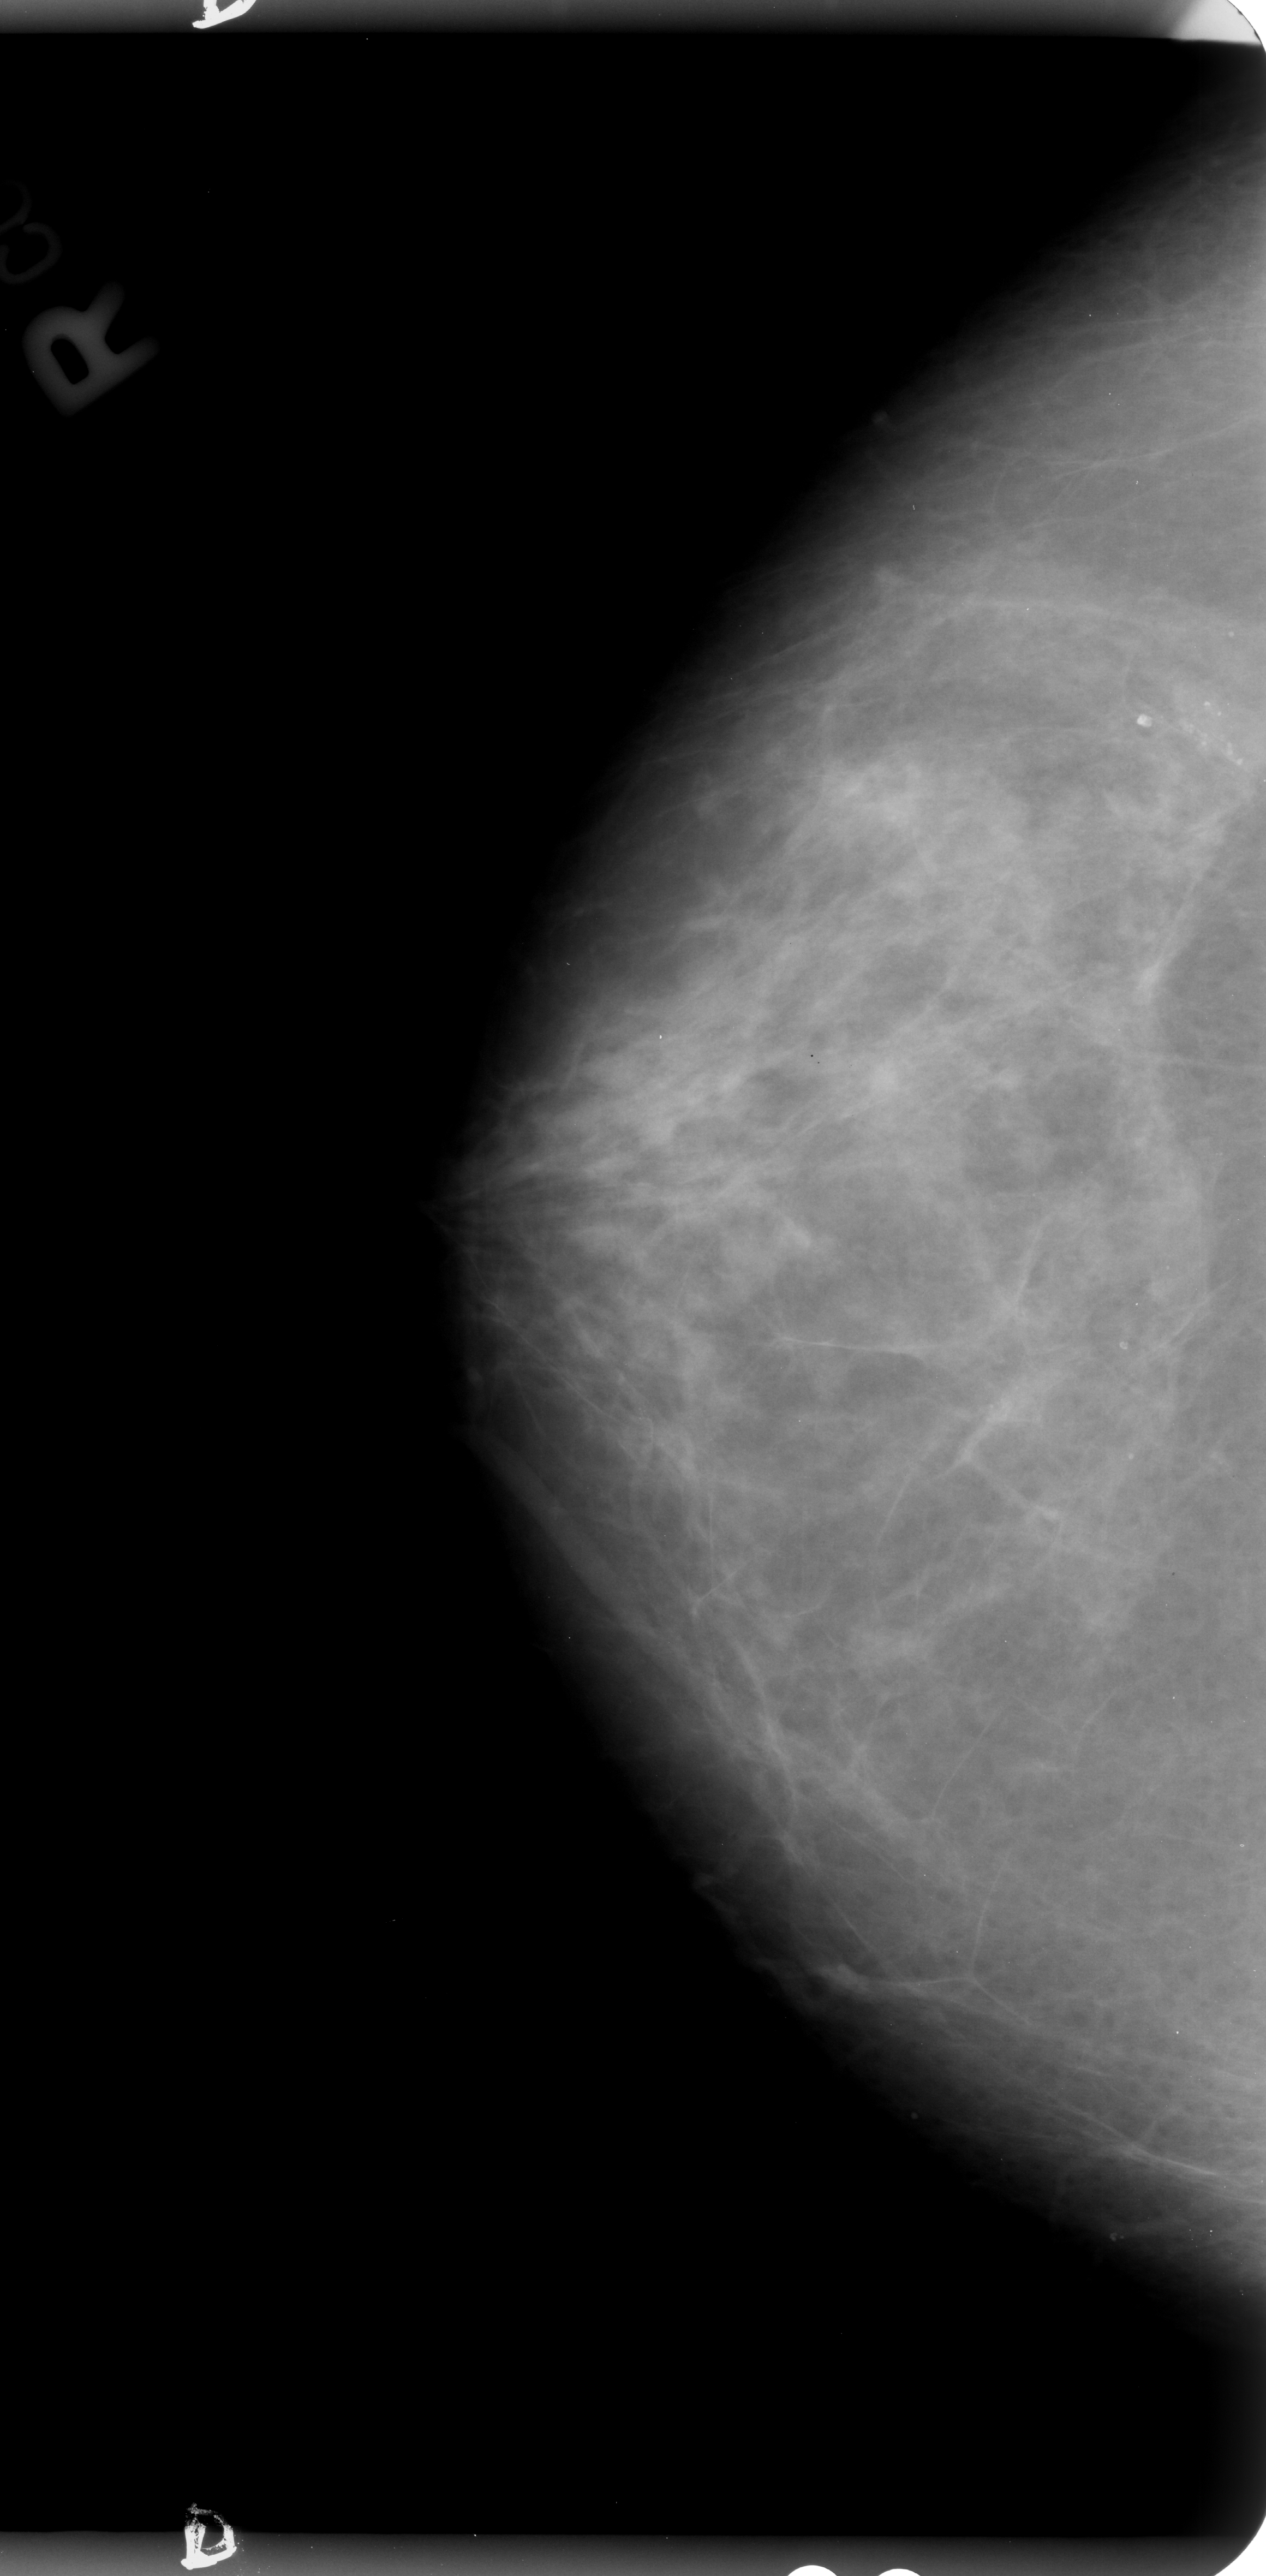
Scanned film-screen mammogram, right breast, CC view, BI-RADS breast density category 2 (scale 1–4).
Marked abnormality: calcifications, morphology pleomorphic, distribution clustered; BI-RADS assessment category 4; pathology (as recorded): benign.